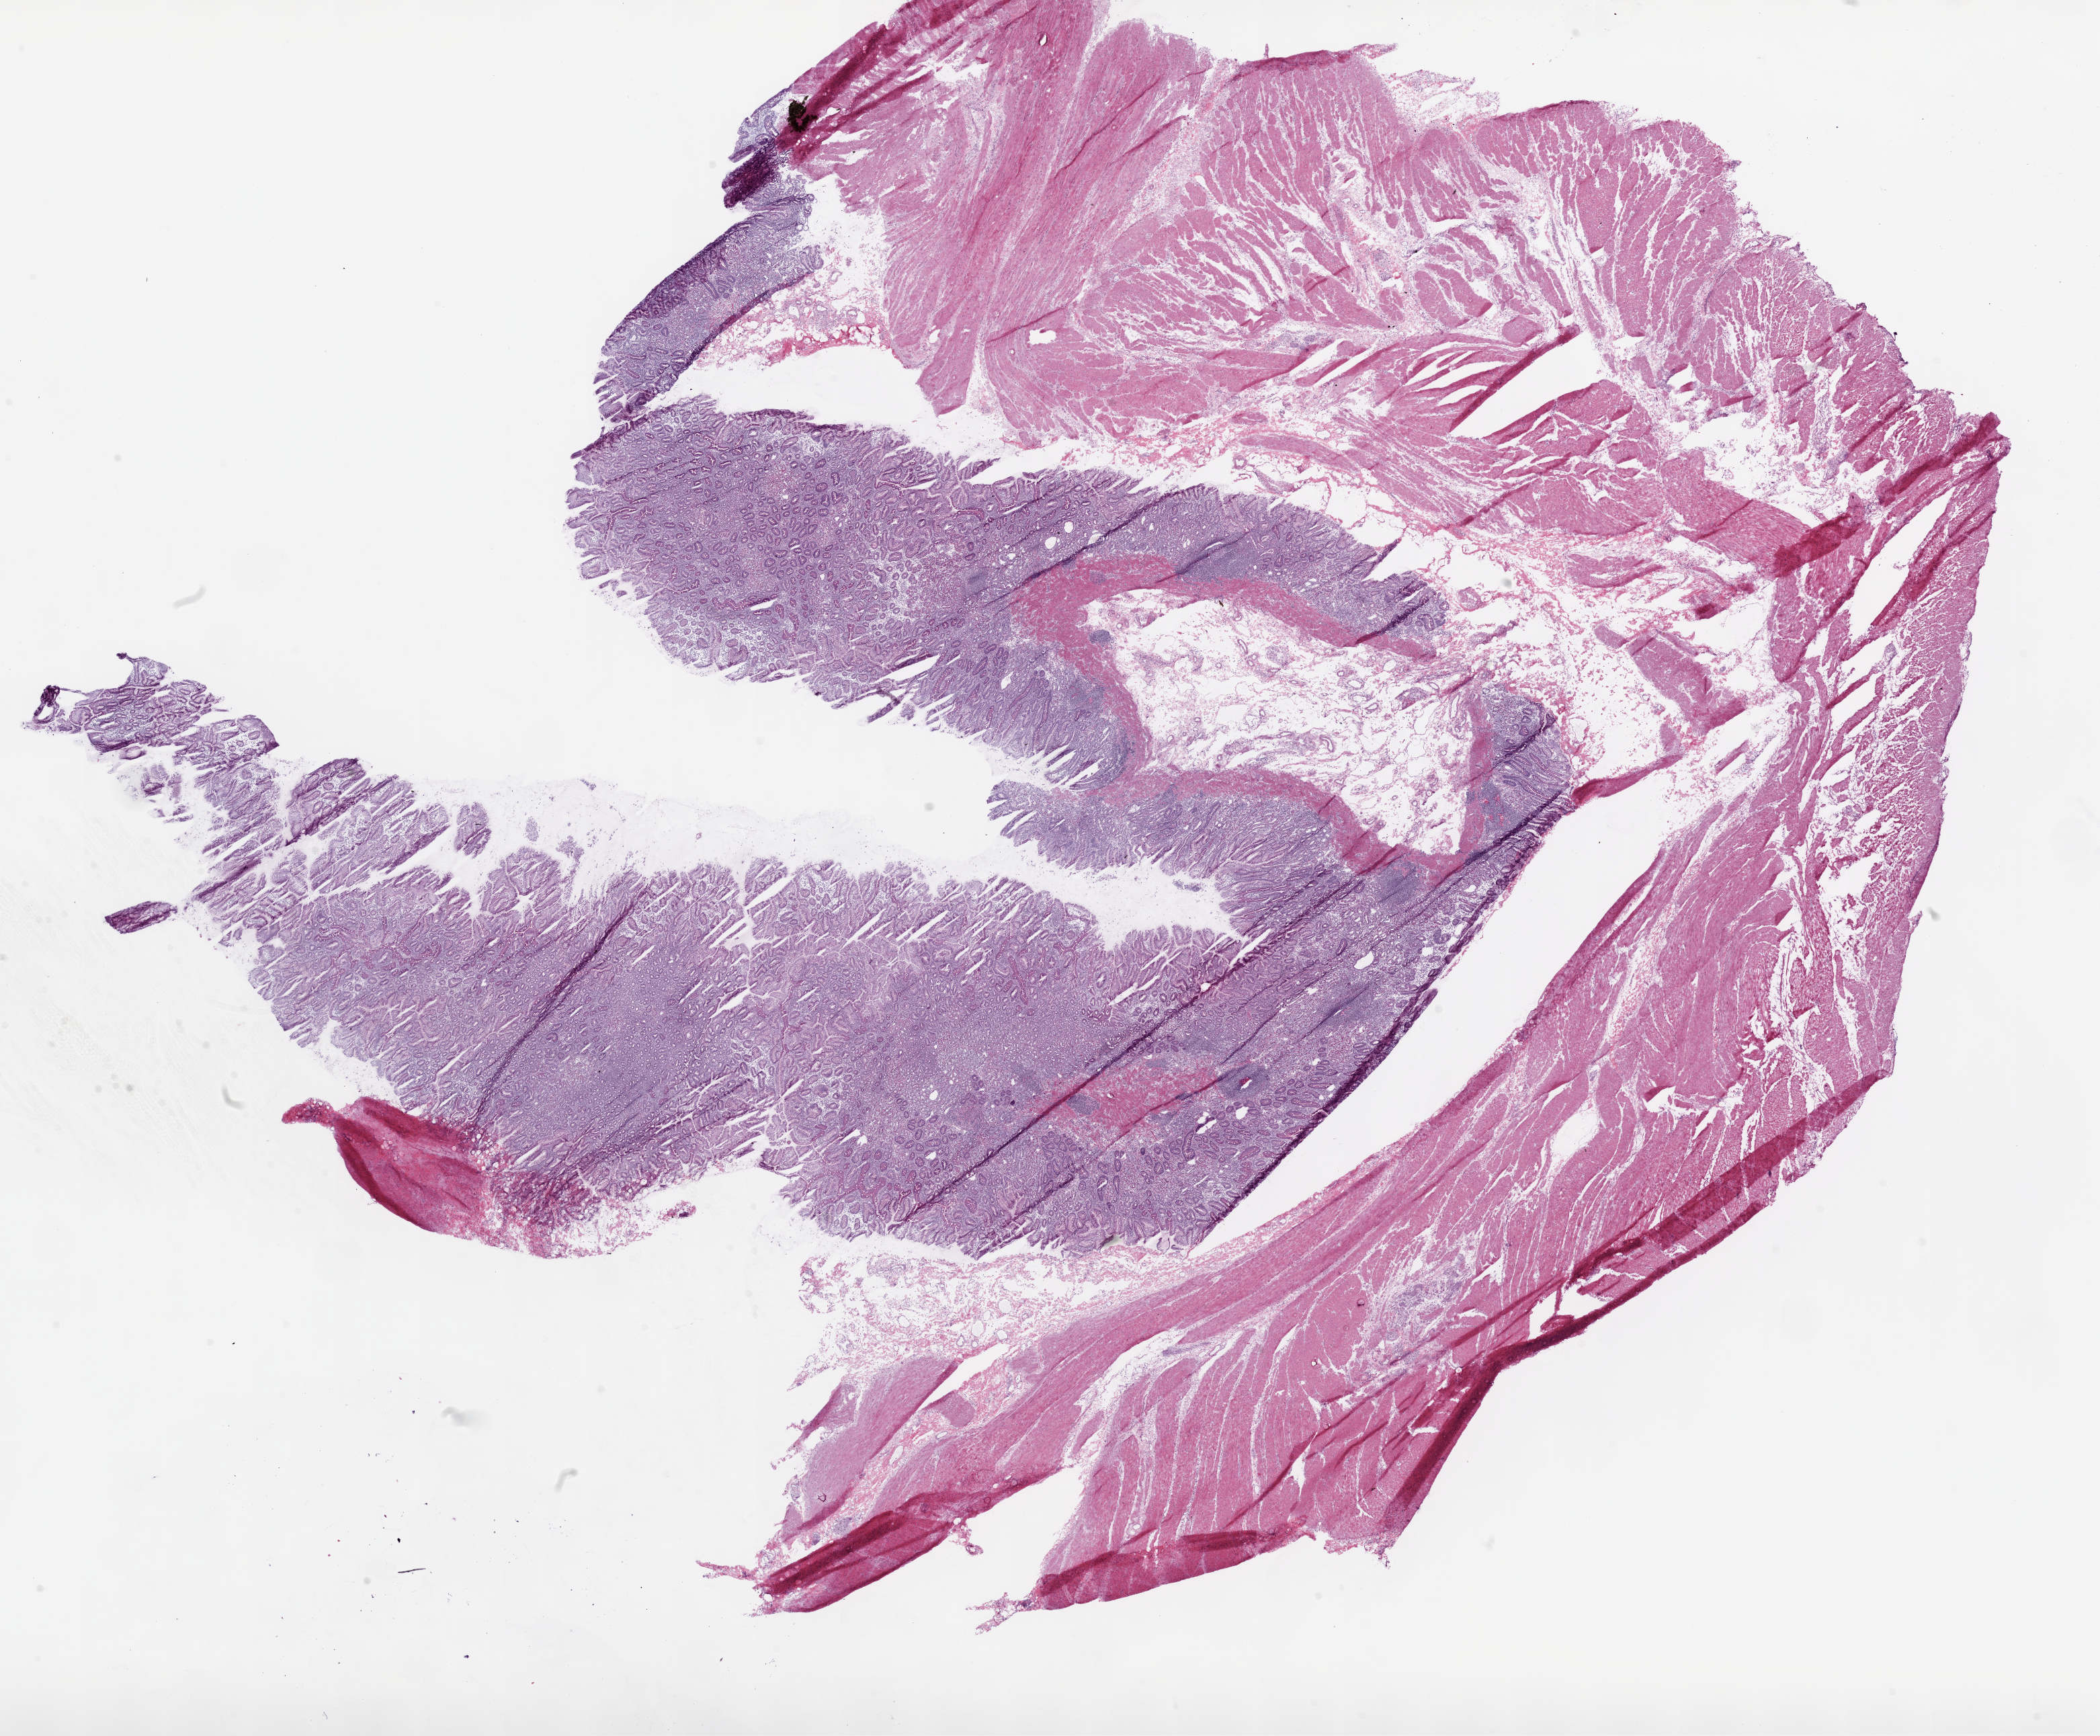
H&E whole-slide image — shown as a low-resolution overview of the whole scanned area (about 25.1 x 20.7 mm, acquisition: 20x scan). Frozen section. Solid tissue normal (non-tumour tissue) sample from the stomach. Male patient; age at initial diagnosis 78 years.
This section: solid tissue normal (non-tumour) sample from the same patient. Patient diagnosis: Adenocarcinoma, NOS (gastric antrum).